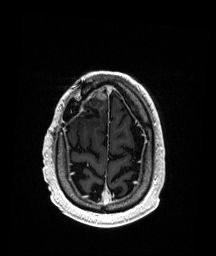
Brain MRI from a brain-tumour surgery series, one axial slice; slice 39 of 192 in the series (ordered by position); T1-weighted post-contrast; 1 mm slice thickness; 216 × 256 image matrix, field of view 211 × 250 mm. From the clinical record (not read from this slice): histopathology: Astrocytoma; WHO grade: 3; IDH mutation: yes; tumour location: Right Frontal.
Annotated regions visible in this slice (outlined manually by an expert reader):
- previous resection cavity: bounding box <79,106,101,118> (left, top, right, bottom; pixels)
- tumour: <93,88,107,100>